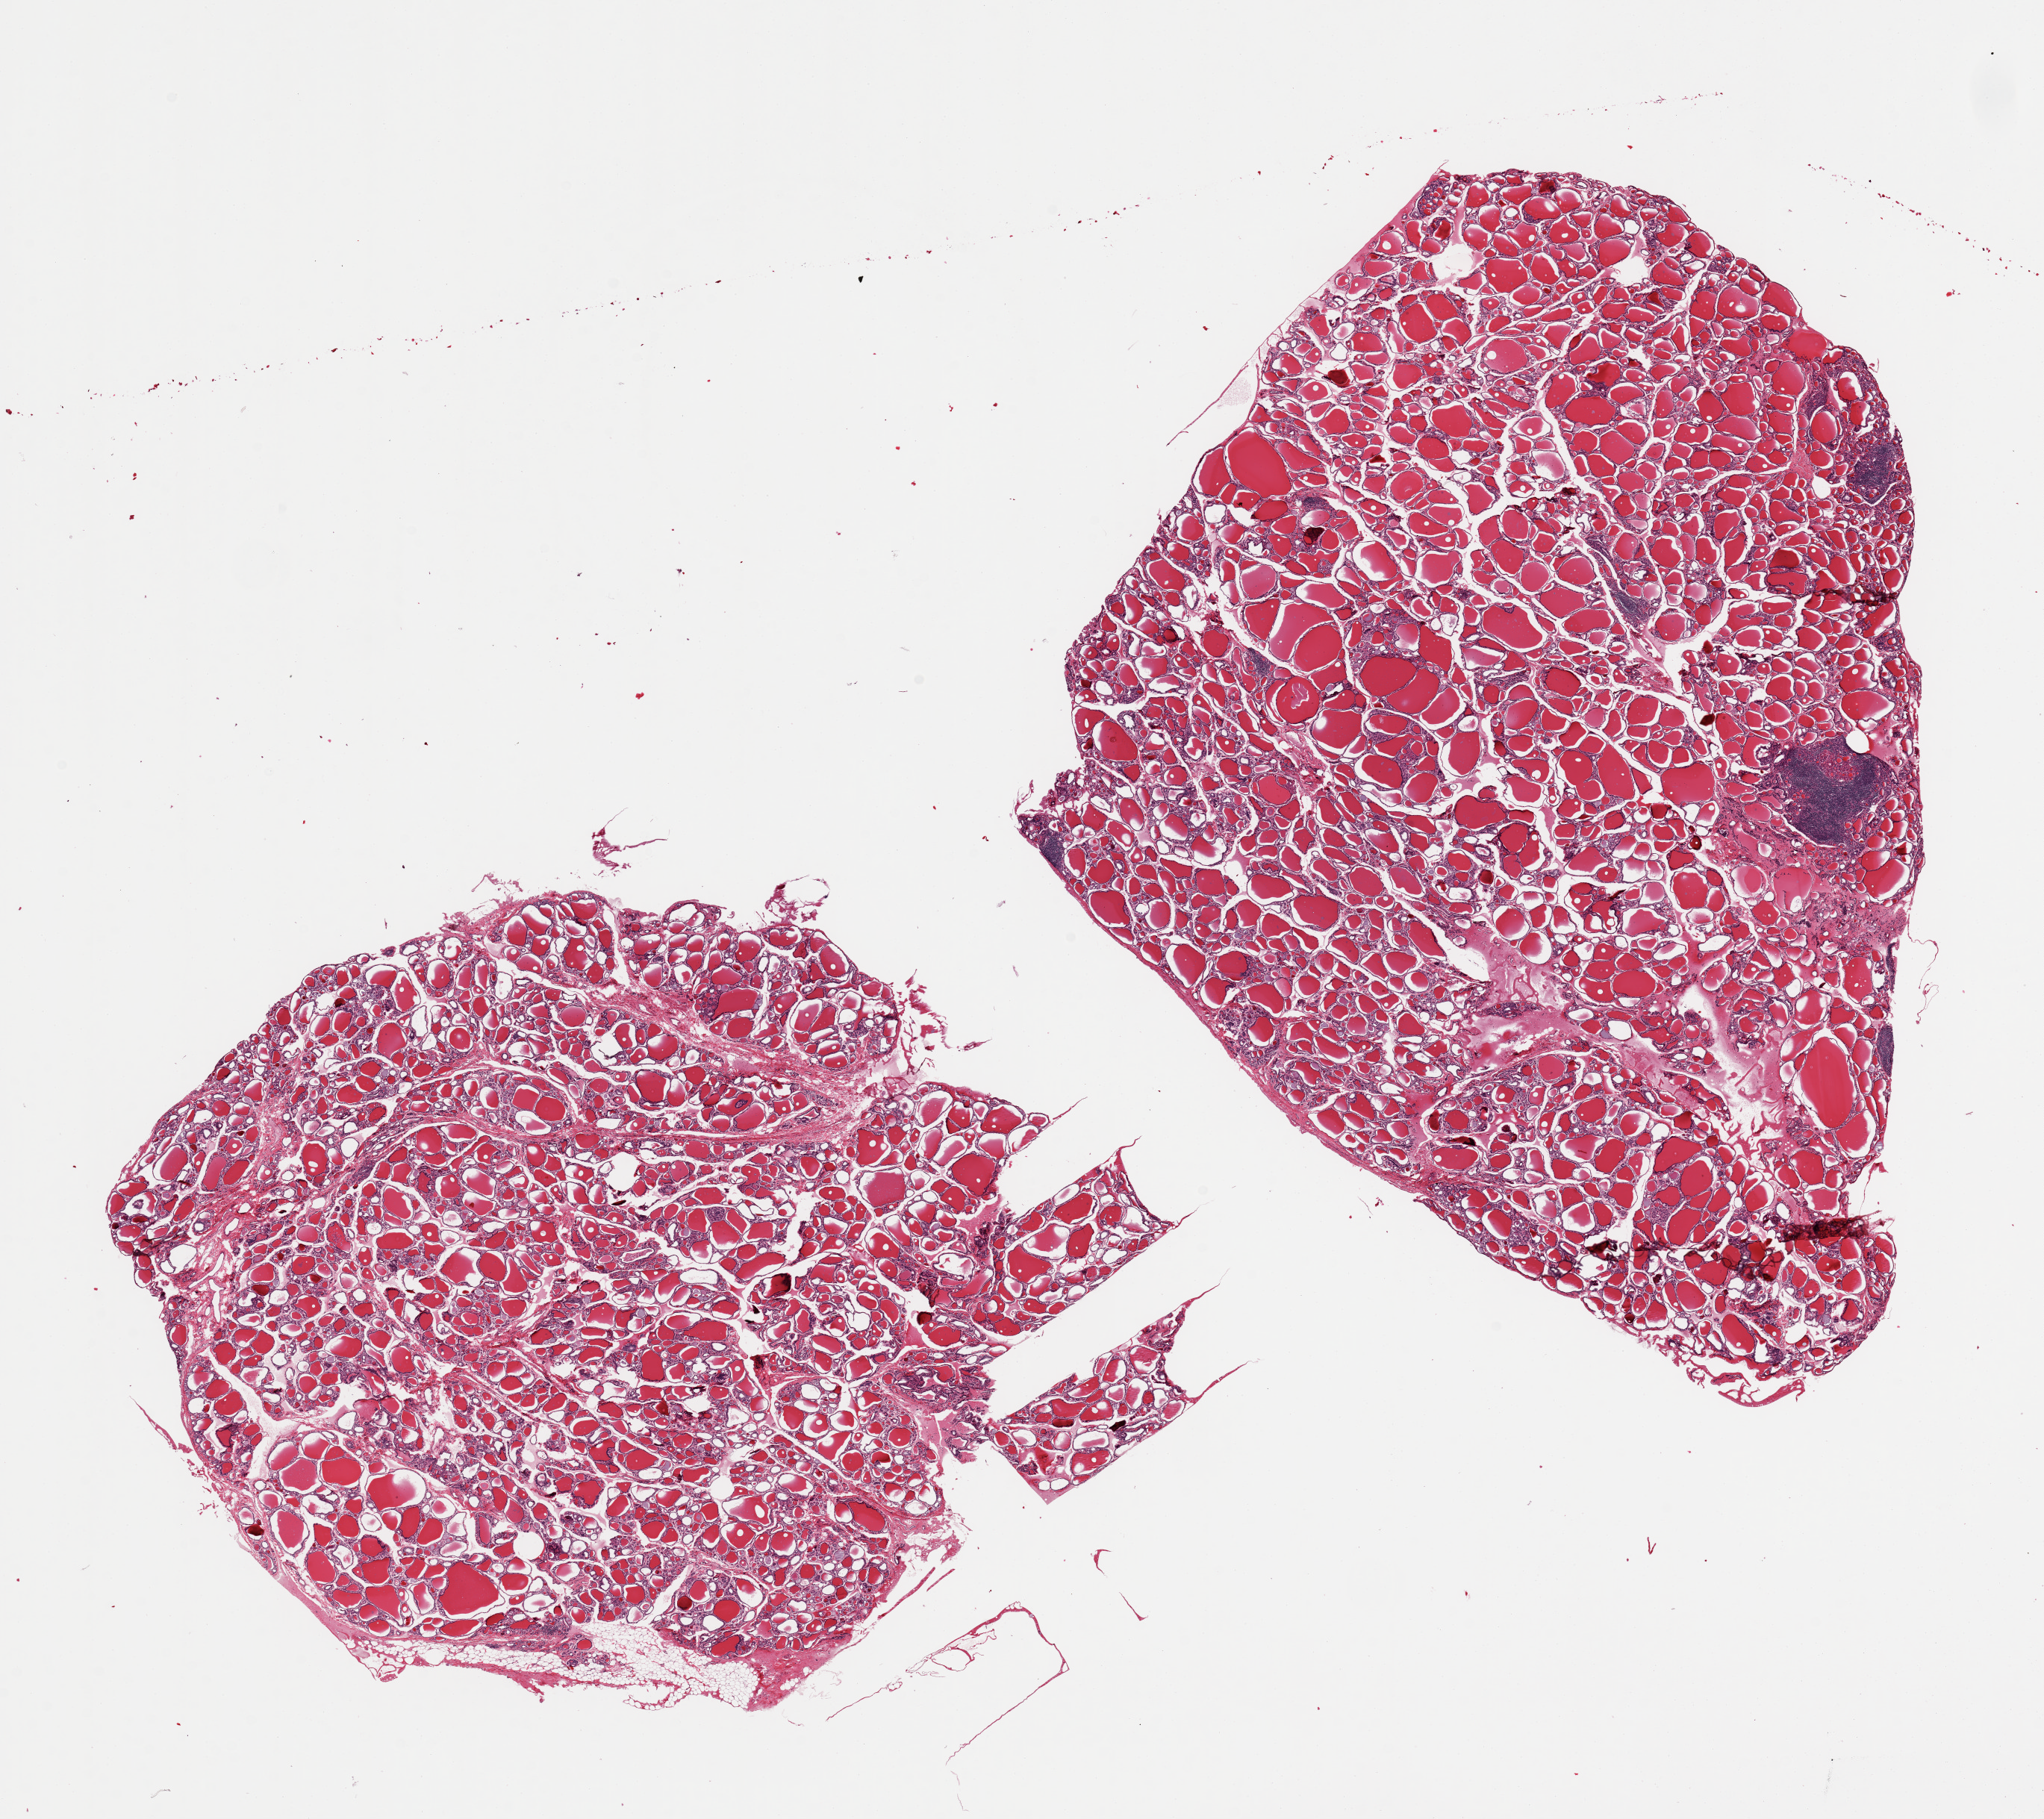
H&E whole-slide image, brightfield, low-resolution overview of the scanned area, about 21.7 x 19.3 mm (from a 20x scan), PAXgene-fixed paraffin-embedded (PFPE) section, section of thyroid (target tissue), donor tissue sample. Male donor.
Review note (as recorded): 2 pieces. Lymphoid nodules of Hashimoto thyroiditis. Foci of C-cell hyperplasia. This along with adrenal medullary hyperplasia raise probability of MEN IIB syndrome.